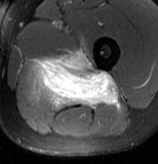
MRI of an extremity soft-tissue mass, one axial slice; slice 49 of 70 in the series (ordered by position); T2-weighted fat-saturated; MR volume resampled by the dataset authors to the PET/CT grid (not the native acquisition matrix); 158 × 164 image matrix, field of view 154 × 160 mm. Male patient. Case-level facts recorded for this patient, not image findings: histological type: extraskeletal osteosarcoma; grade: high; site of the primary tumour: left adductur.
Annotated regions visible in this slice (expert contour drawn on MRI and transferred to this co-registered scan by the dataset authors):
- gross tumour volume (mass): bounding box <31,50,119,109> (left, top, right, bottom; pixels)